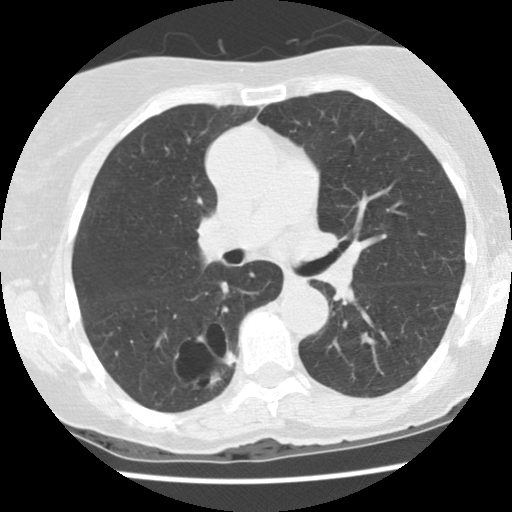
Low-dose screening chest CT, one axial slice. Slice 83 of 136 in the series (ordered by position). 120 kVp. Lung window (W 1500 / L -600 HU). 512 × 512 image matrix, field of view 300 × 300 mm.
Outlined on this slice (expert manual segmentation):
- lesion 1 (tumor, lower lobe of right lung): bounding box <211,352,236,382> (left, top, right, bottom; pixels)